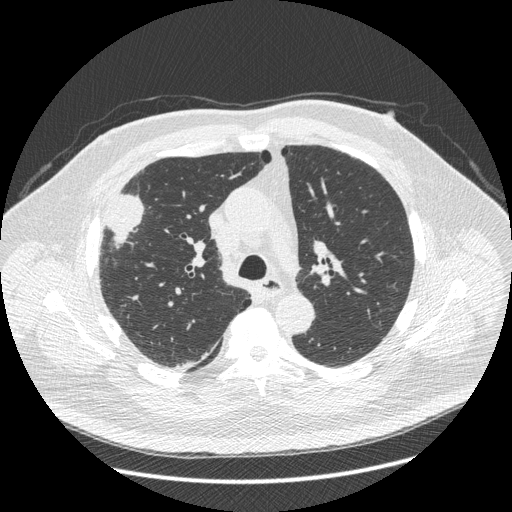
Low-dose screening chest CT, one axial slice; slice 286 of 426 in the series (ordered by position); lung window (W 1500 / L -600 HU); 1.25 mm slice thickness; 512 × 512 image matrix, field of view 400 × 400 mm.
Structures marked on this image (expert manual segmentation):
- lesion 1 (tumor, upper lobe of right lung): bounding box [x1, y1, x2, y2] px = [106, 194, 143, 246]